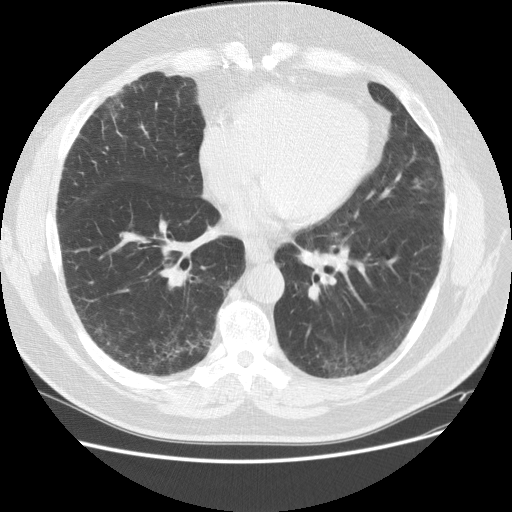
Low-dose screening chest CT, axial slice, baseline screening round, lung window (W 1500 / L -600 HU), 2.5 mm slice thickness, standard (soft-tissue) reconstruction kernel (STANDARD). Male participant, aged 59 years at enrolment.
Expert reader's lesion annotation, bounding box <85,83,131,136> (left, top, right, bottom; pixels). The screening reader recorded 2 non-calcified nodules or masses ≥4 mm on this exam (right middle lobe, right lower lobe); which of them this box marks is not recorded. Participant outcome: lung cancer diagnosed 338 days after this screen — adenocarcinoma, NOS, right upper lobe, right middle lobe, moderately differentiated (G2), stage IA (AJCC 6th edition), 13 mm at pathology.